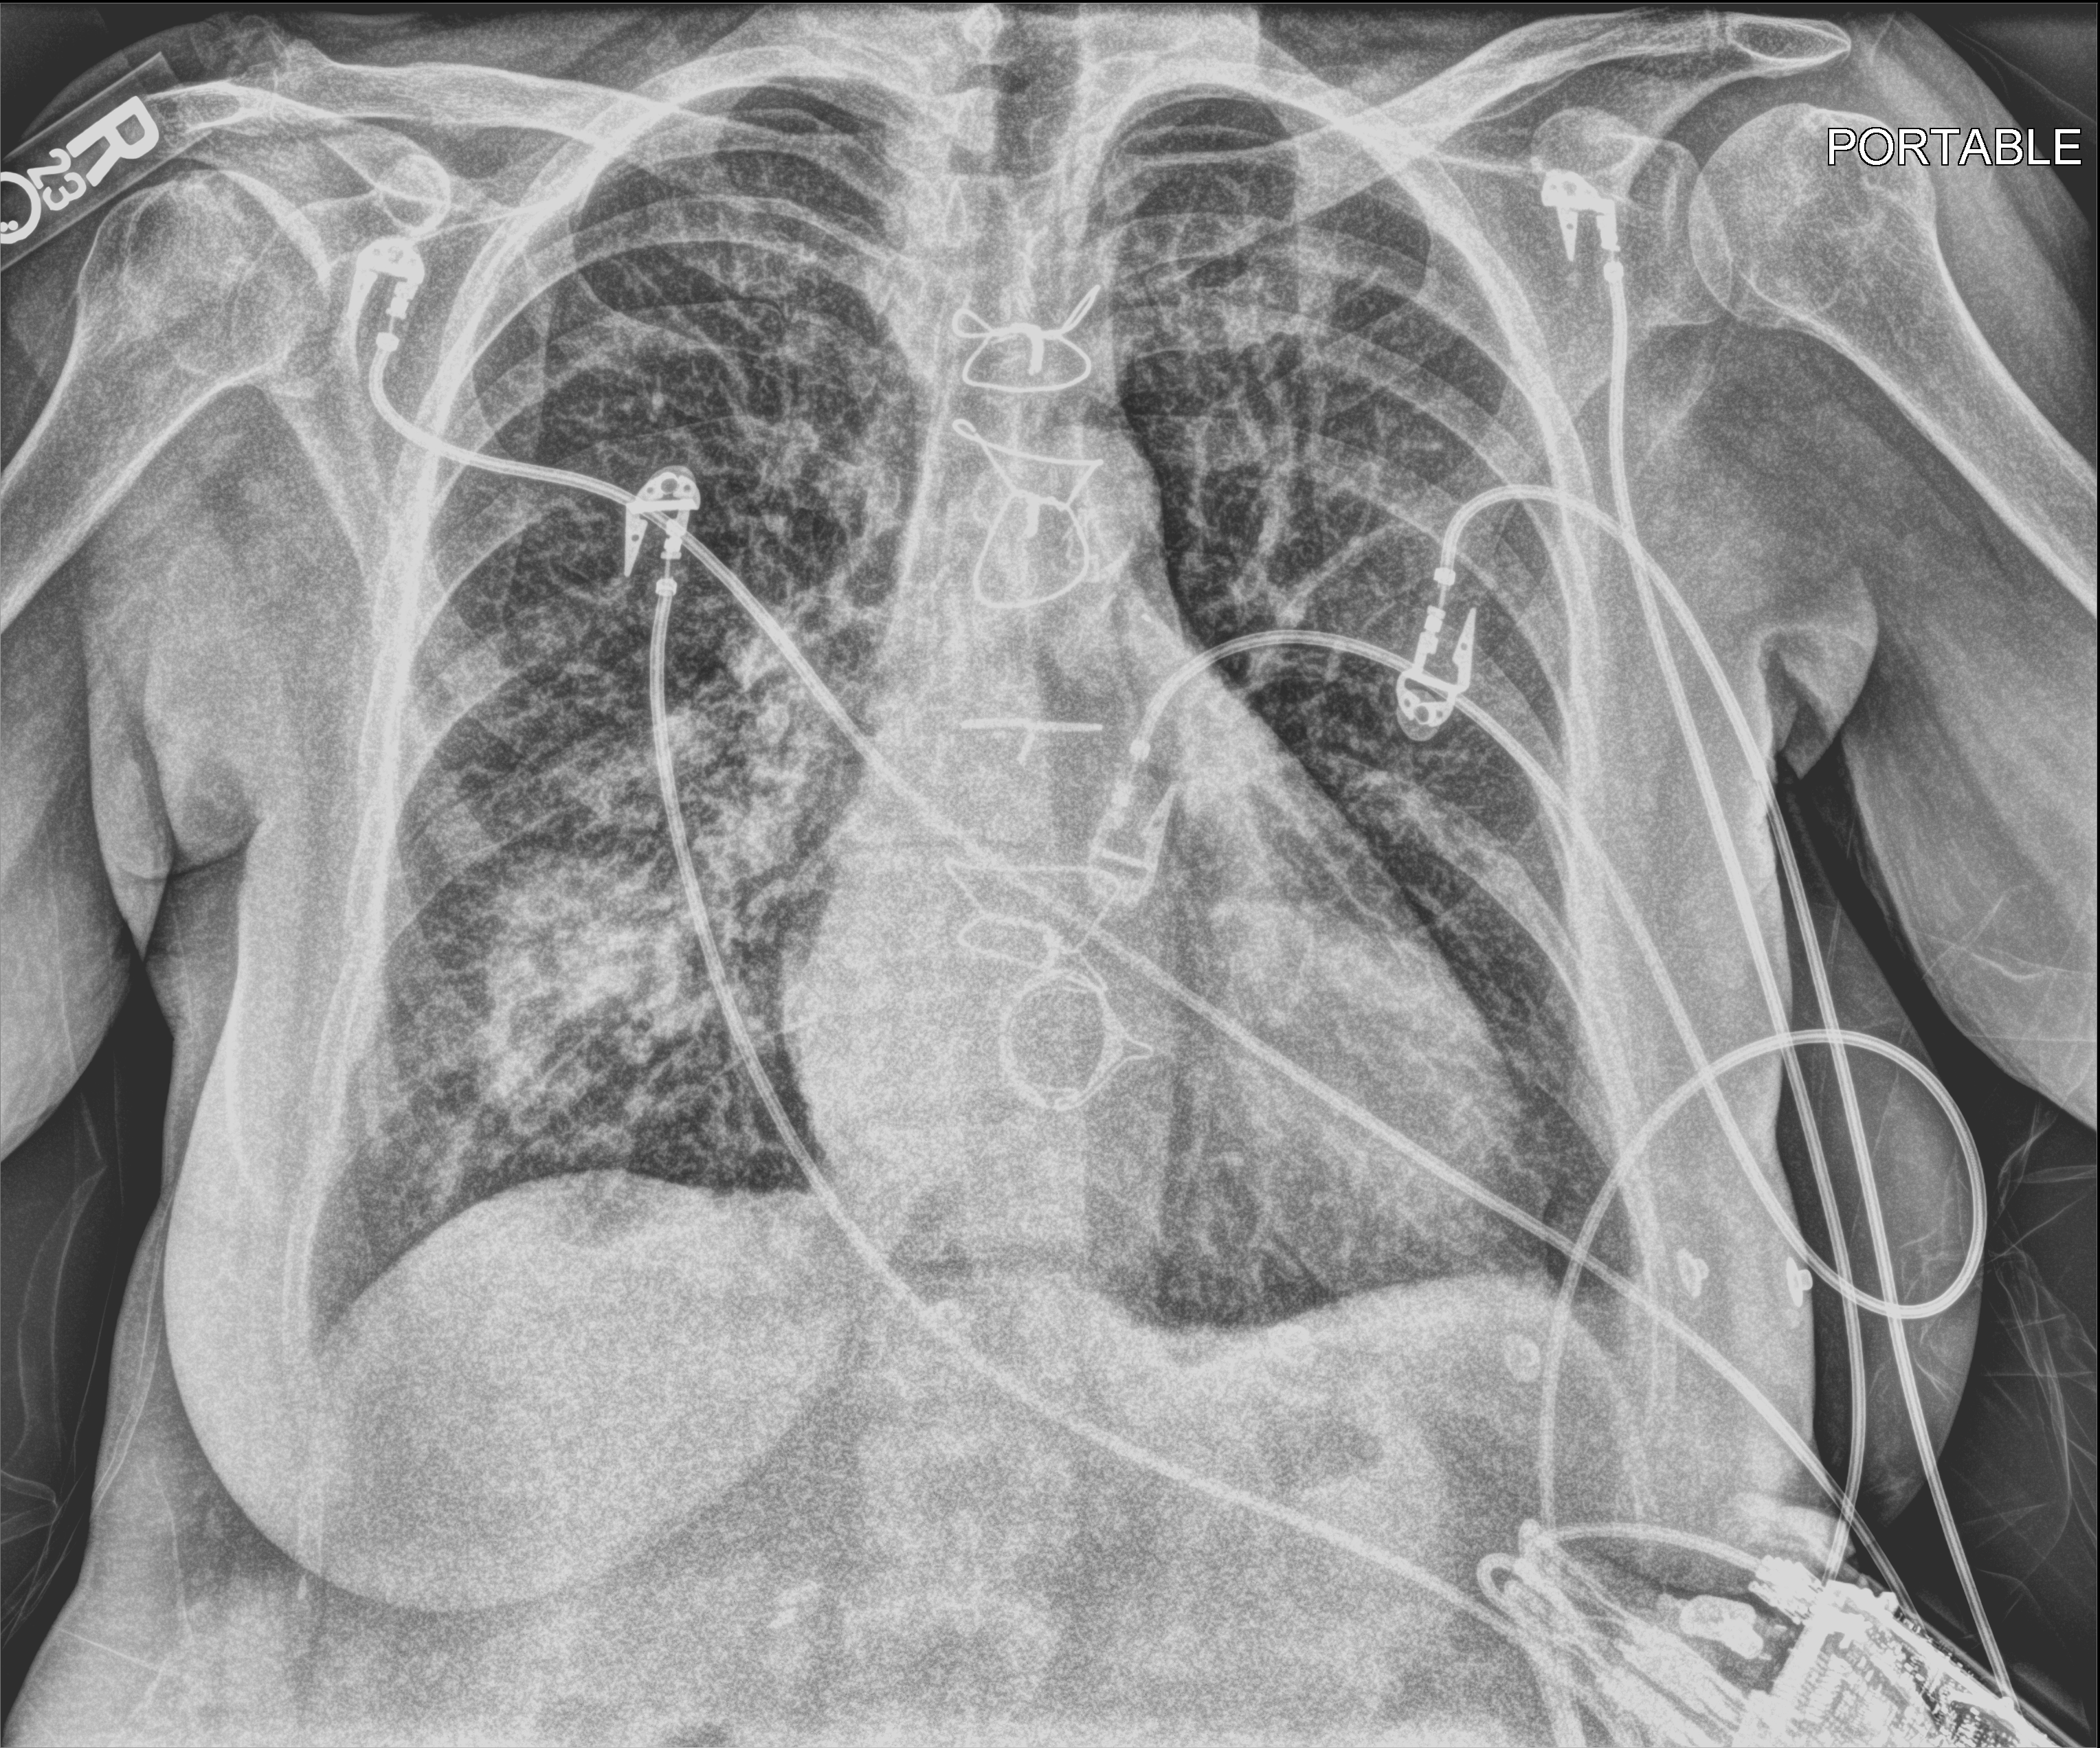
Portable chest radiograph. Patient hospitalised with COVID-19; female, aged 60–74 years.
From the hospital-stay record, not from the radiograph (when in the stay this image was taken is not recorded): admitted to intensive care during this hospital stay: yes.